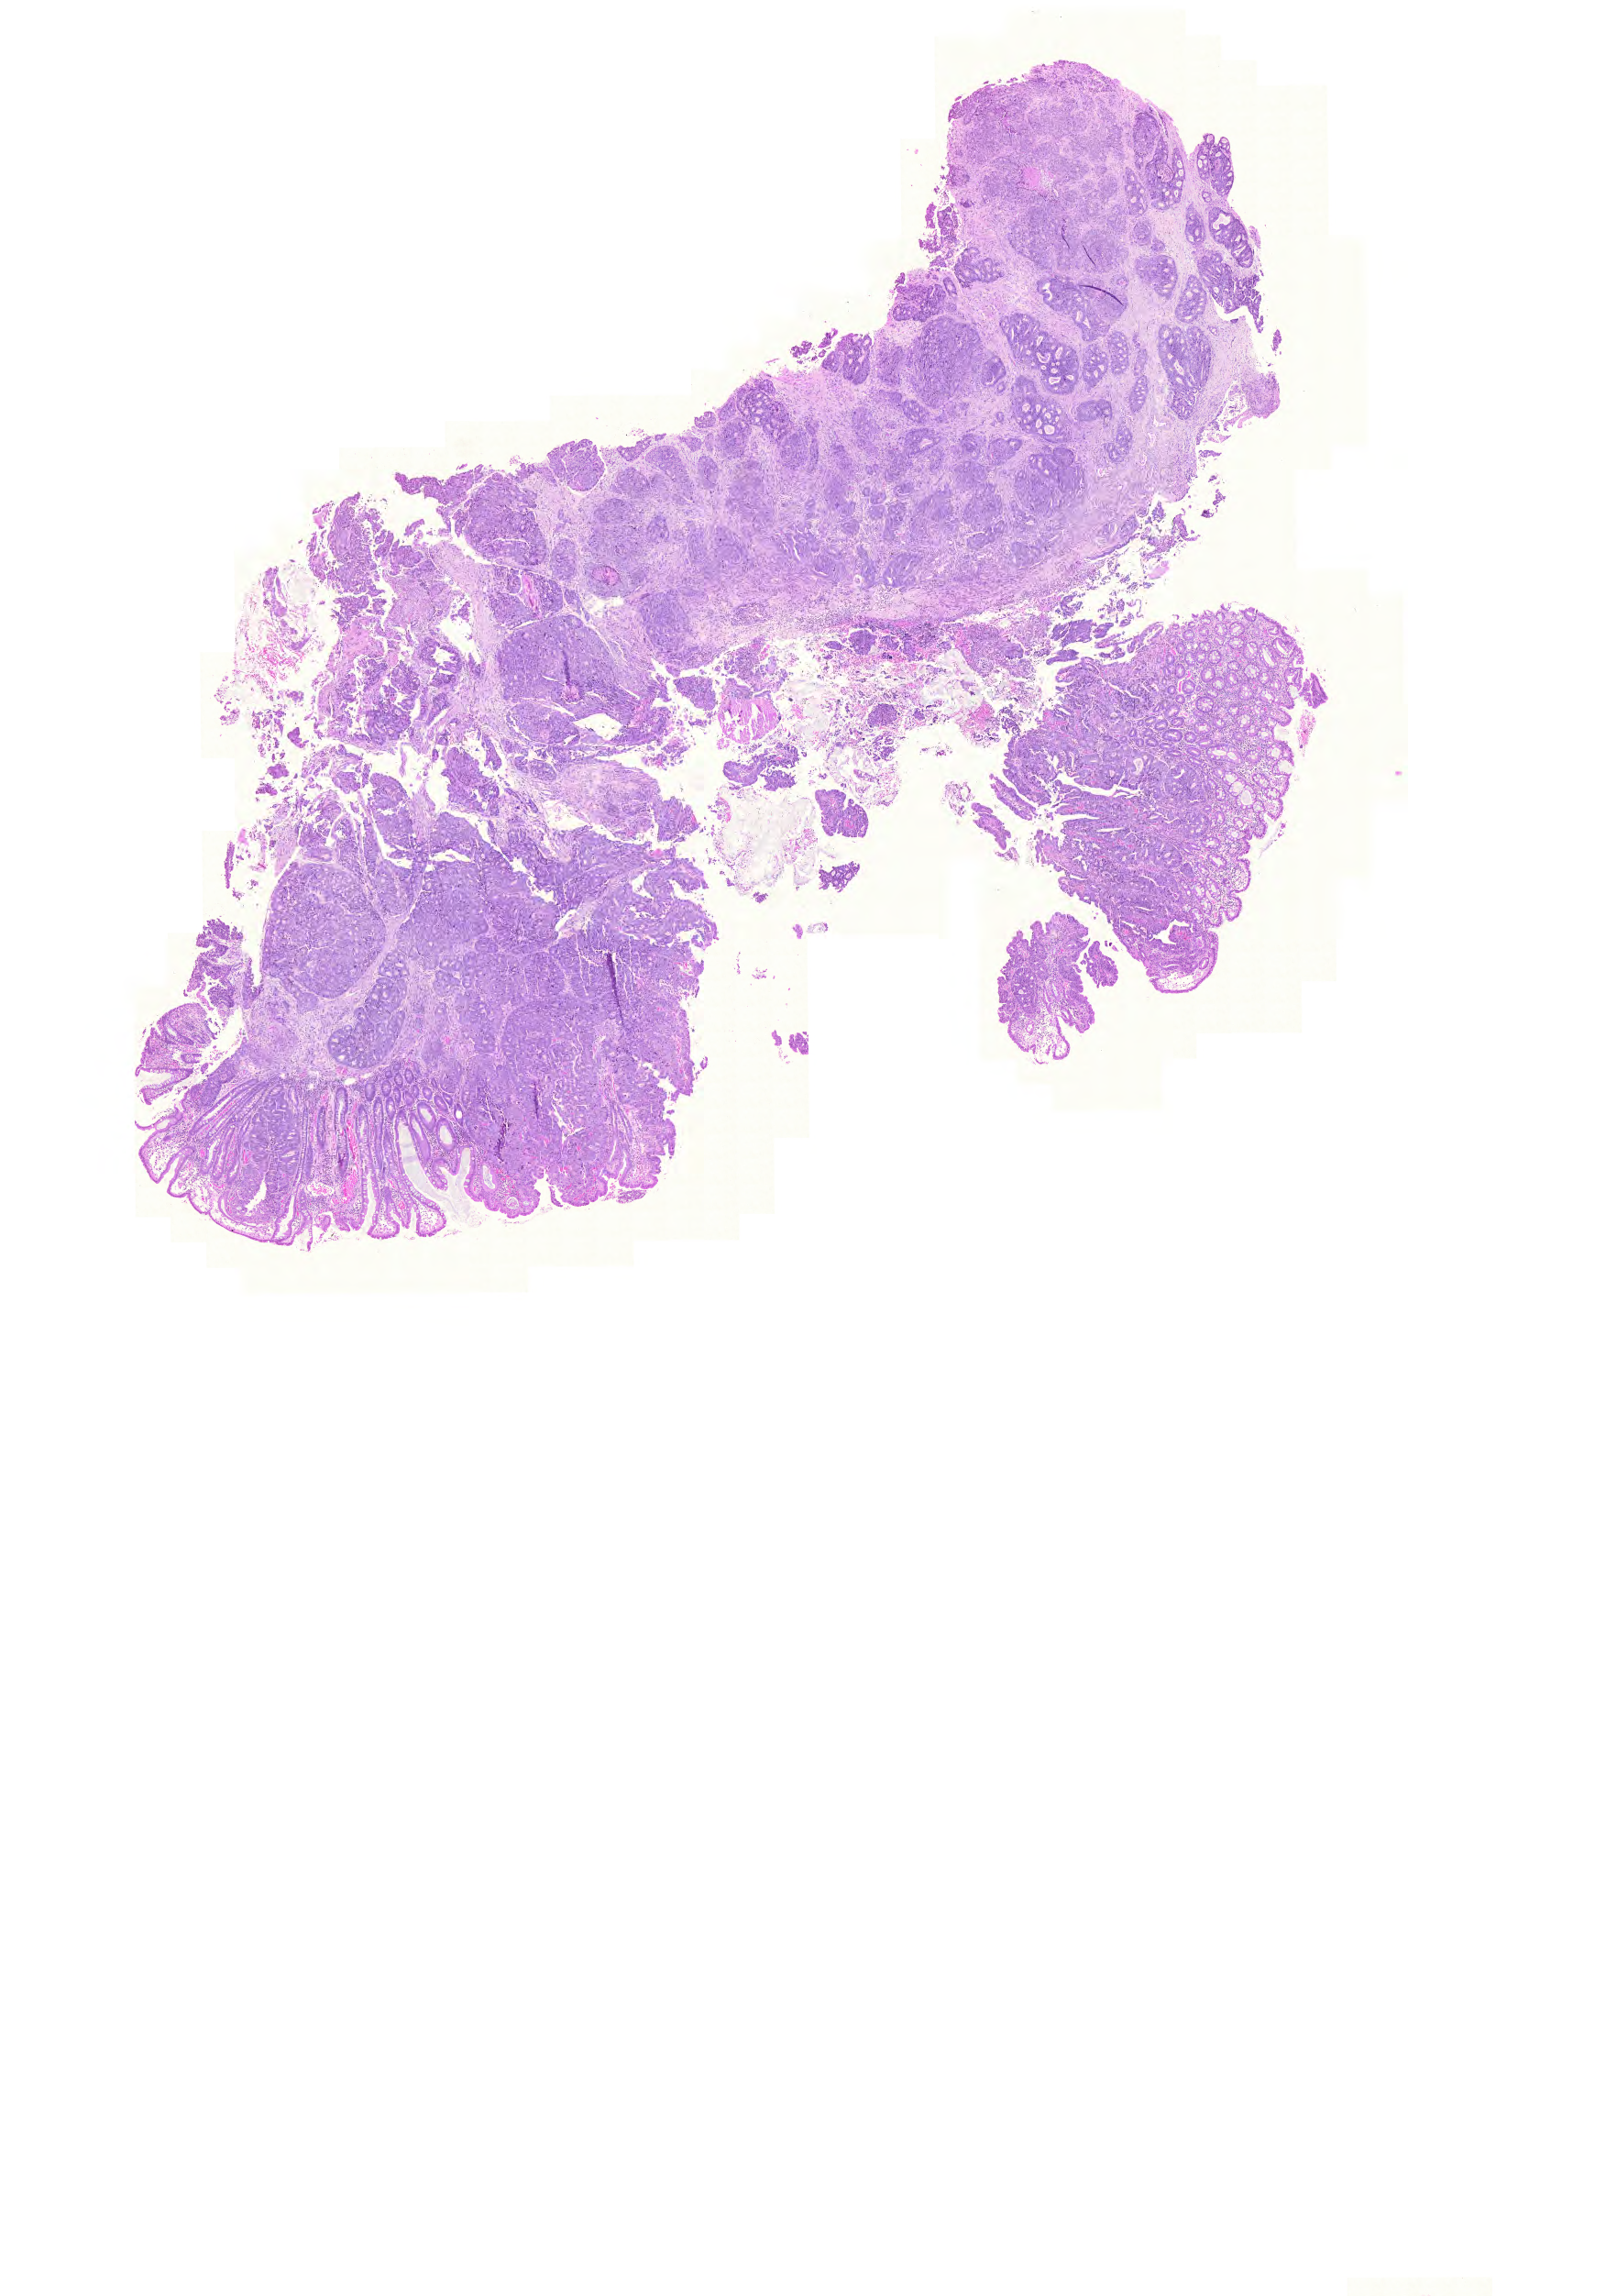
Digitized Hematoxylin and eosin (H&E) stained tissue section (whole slide), low-resolution overview of the scanned area, about 13.0 x 18.6 mm; FFPE section; colon, primary tumour sample. Male patient; age at initial diagnosis 59 years.
Lymph nodes positive (case pathology): 5 of 12 examined. Histologic diagnosis: Adenocarcinoma, NOS. AJCC pathologic stage: IV (6th edition). TNM: T3 N2 M1.